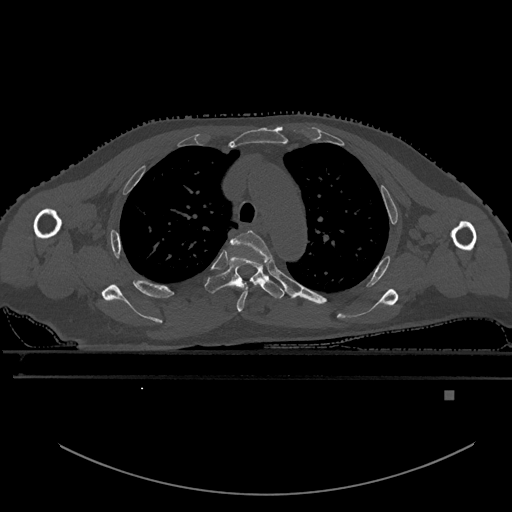
CT including the spine, one axial slice. Slice 422 of 969 in the series (ordered by position). Bone window (W 1800 / L 400 HU). 0.5 mm slice thickness. 512 × 512 image matrix. Patient: male, 82 years. From the clinical record (not read from this slice): primary cancer: prostate.
Structures marked on this image (semi-automatically segmented with operator editing):
- T3 vertebra: box from (x=231, y=230) to (x=273, y=312) px
- T4 vertebra: (x=205, y=255)–(x=285, y=299)